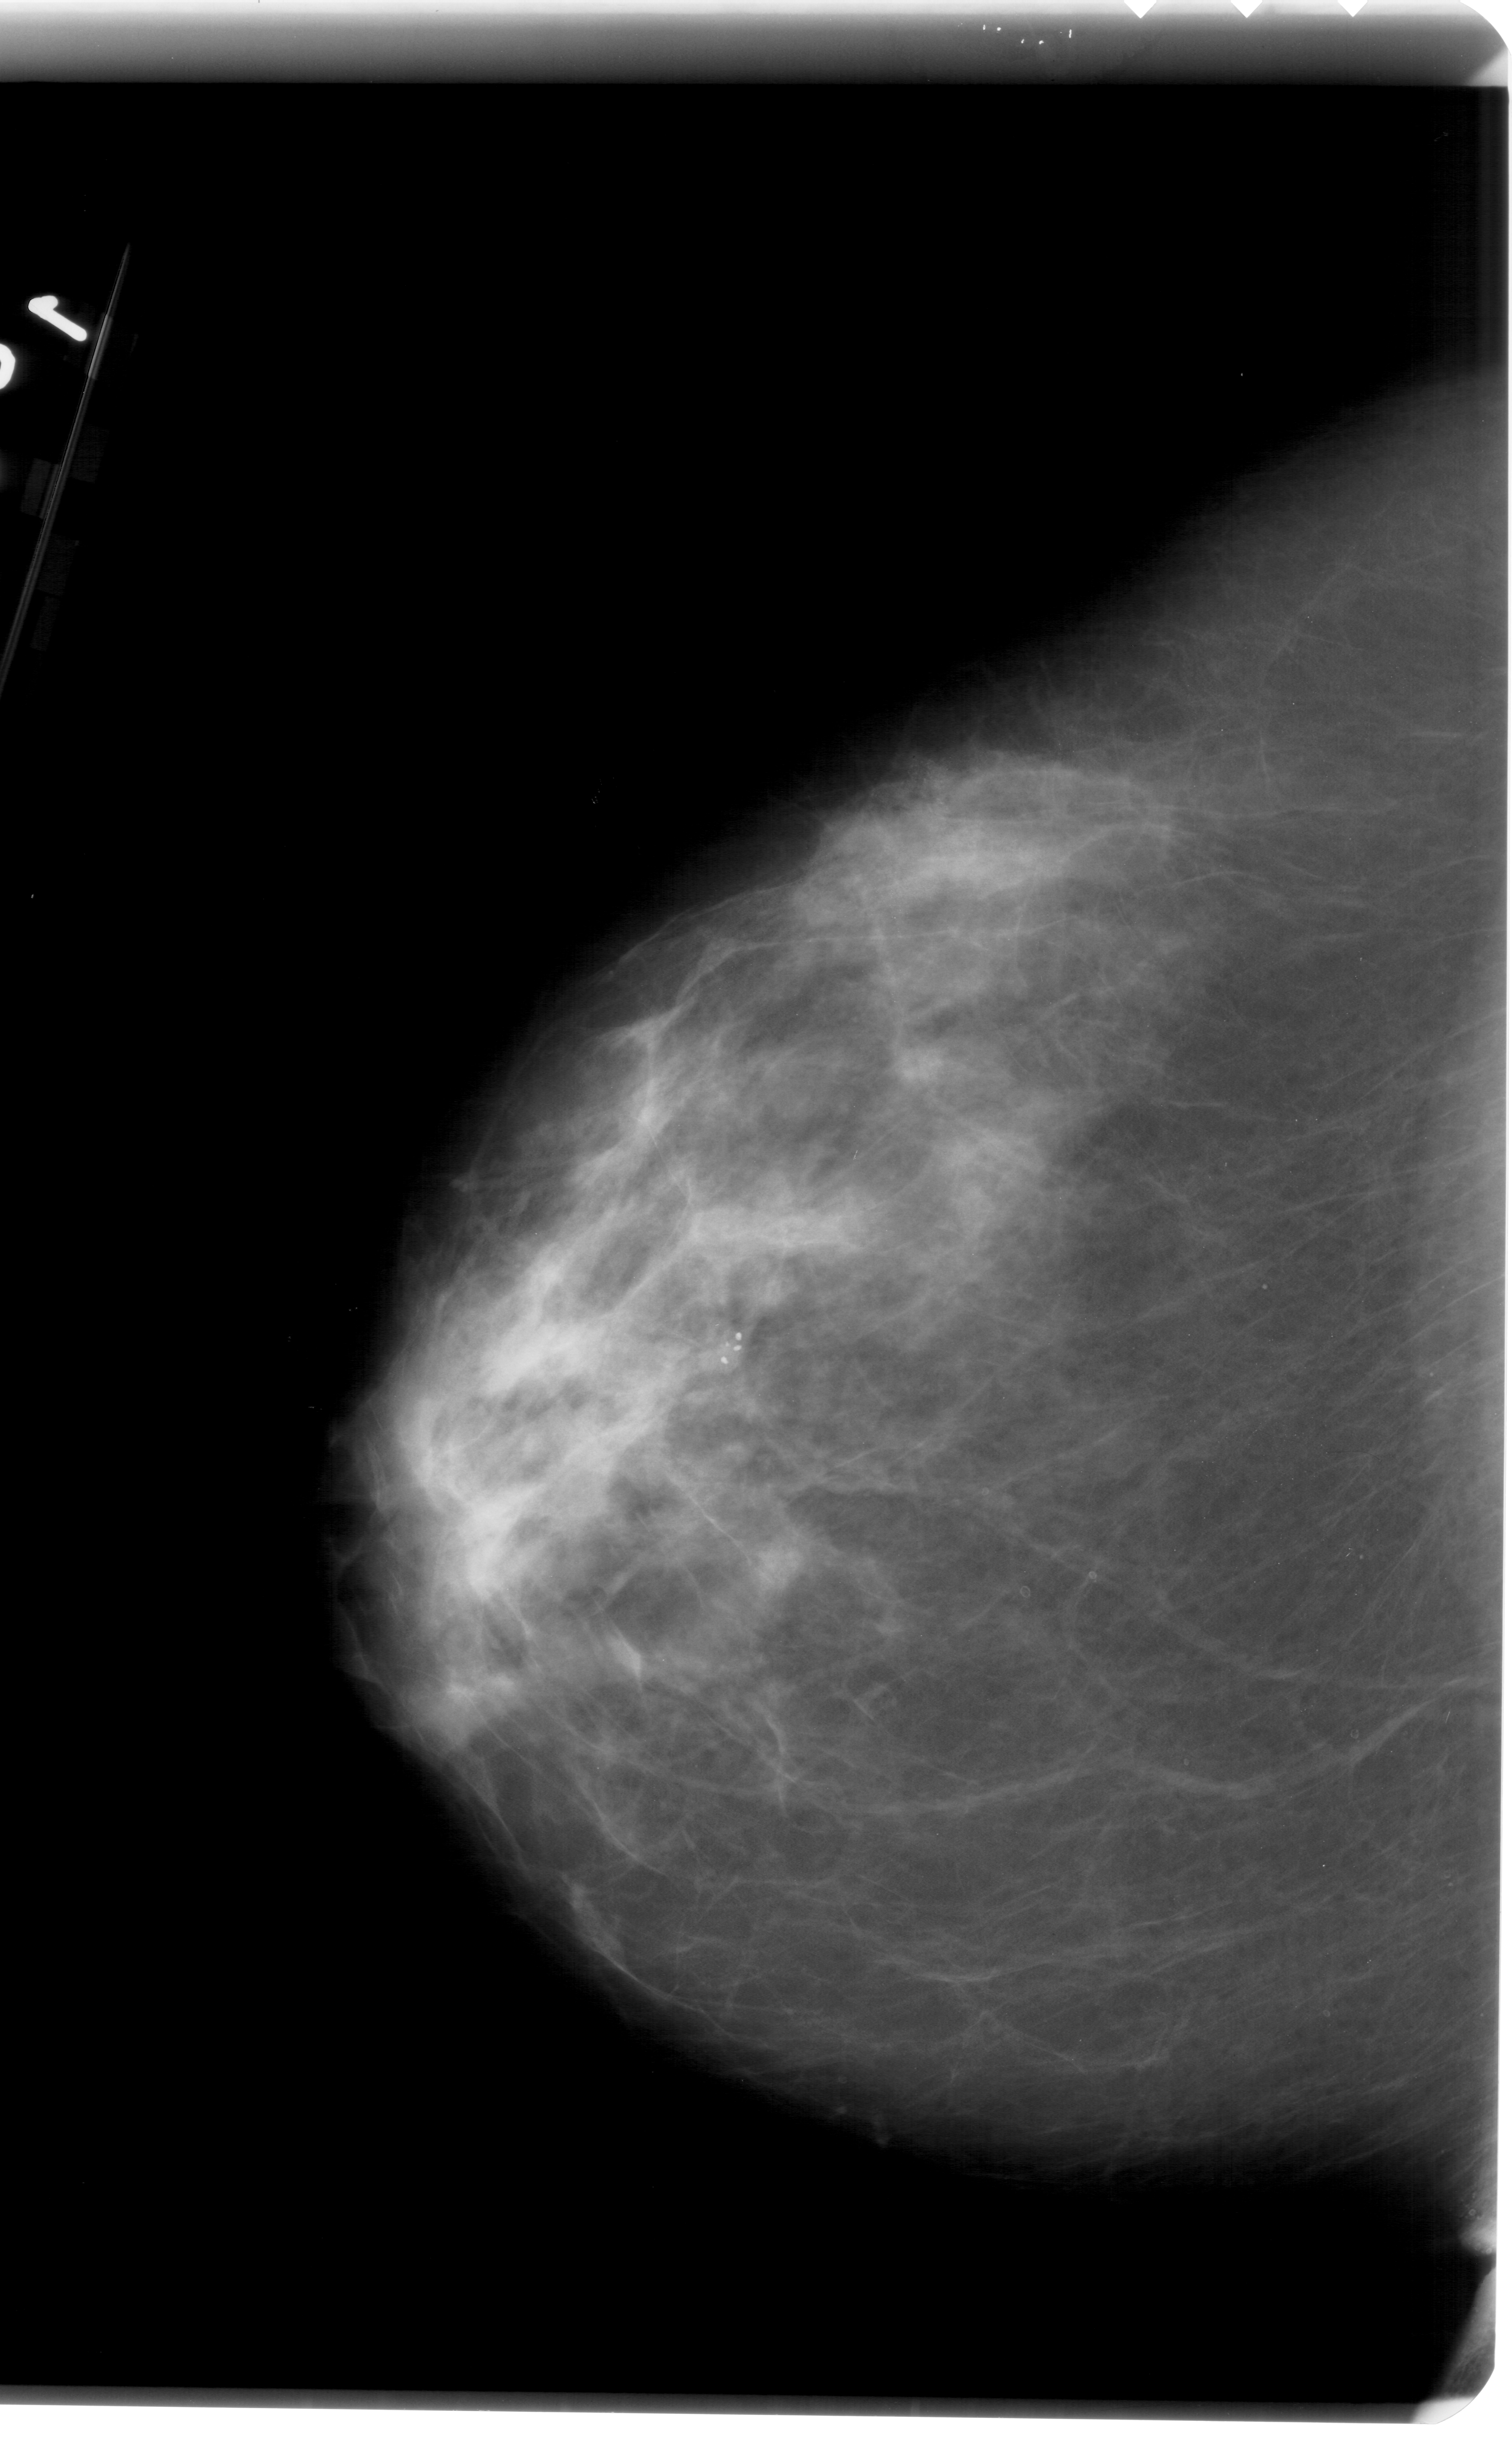
Scanned film-screen mammogram; left breast; craniocaudal (CC) view; breast composition: extremely dense (BI-RADS density category 4 of 4).
Calcifications, morphology pleomorphic, distribution clustered; BI-RADS assessment category 4; subtlety rating 2 on a 1 (subtle) to 5 (obvious) scale; pathology (as recorded): malignant.